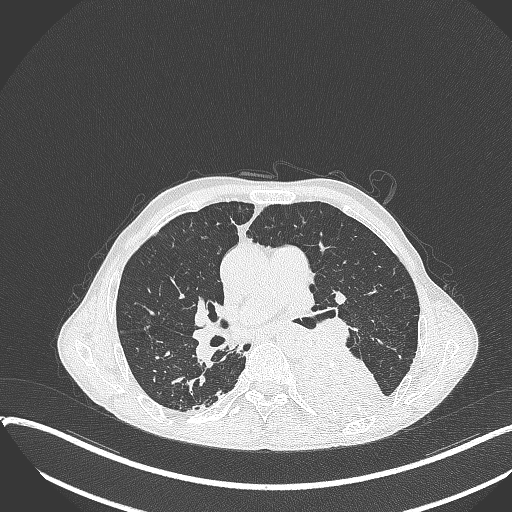
Chest CT, one axial slice; position 213 of 401 along the scan axis; reconstruction kernel B70f; lung window (W 1500 / L -600 HU); 512 × 512 image matrix, field of view 400 × 400 mm. Patient: male, 57 years. Case-level facts recorded for this patient, not image findings: clinical TNM (as recorded): T4 N0 M0.
Annotated regions visible in this slice (rectangle marked by the reading radiologist):
- lung tumour (recorded histology: squamous cell carcinoma): bounding box <293,343,392,430> (left, top, right, bottom; pixels)